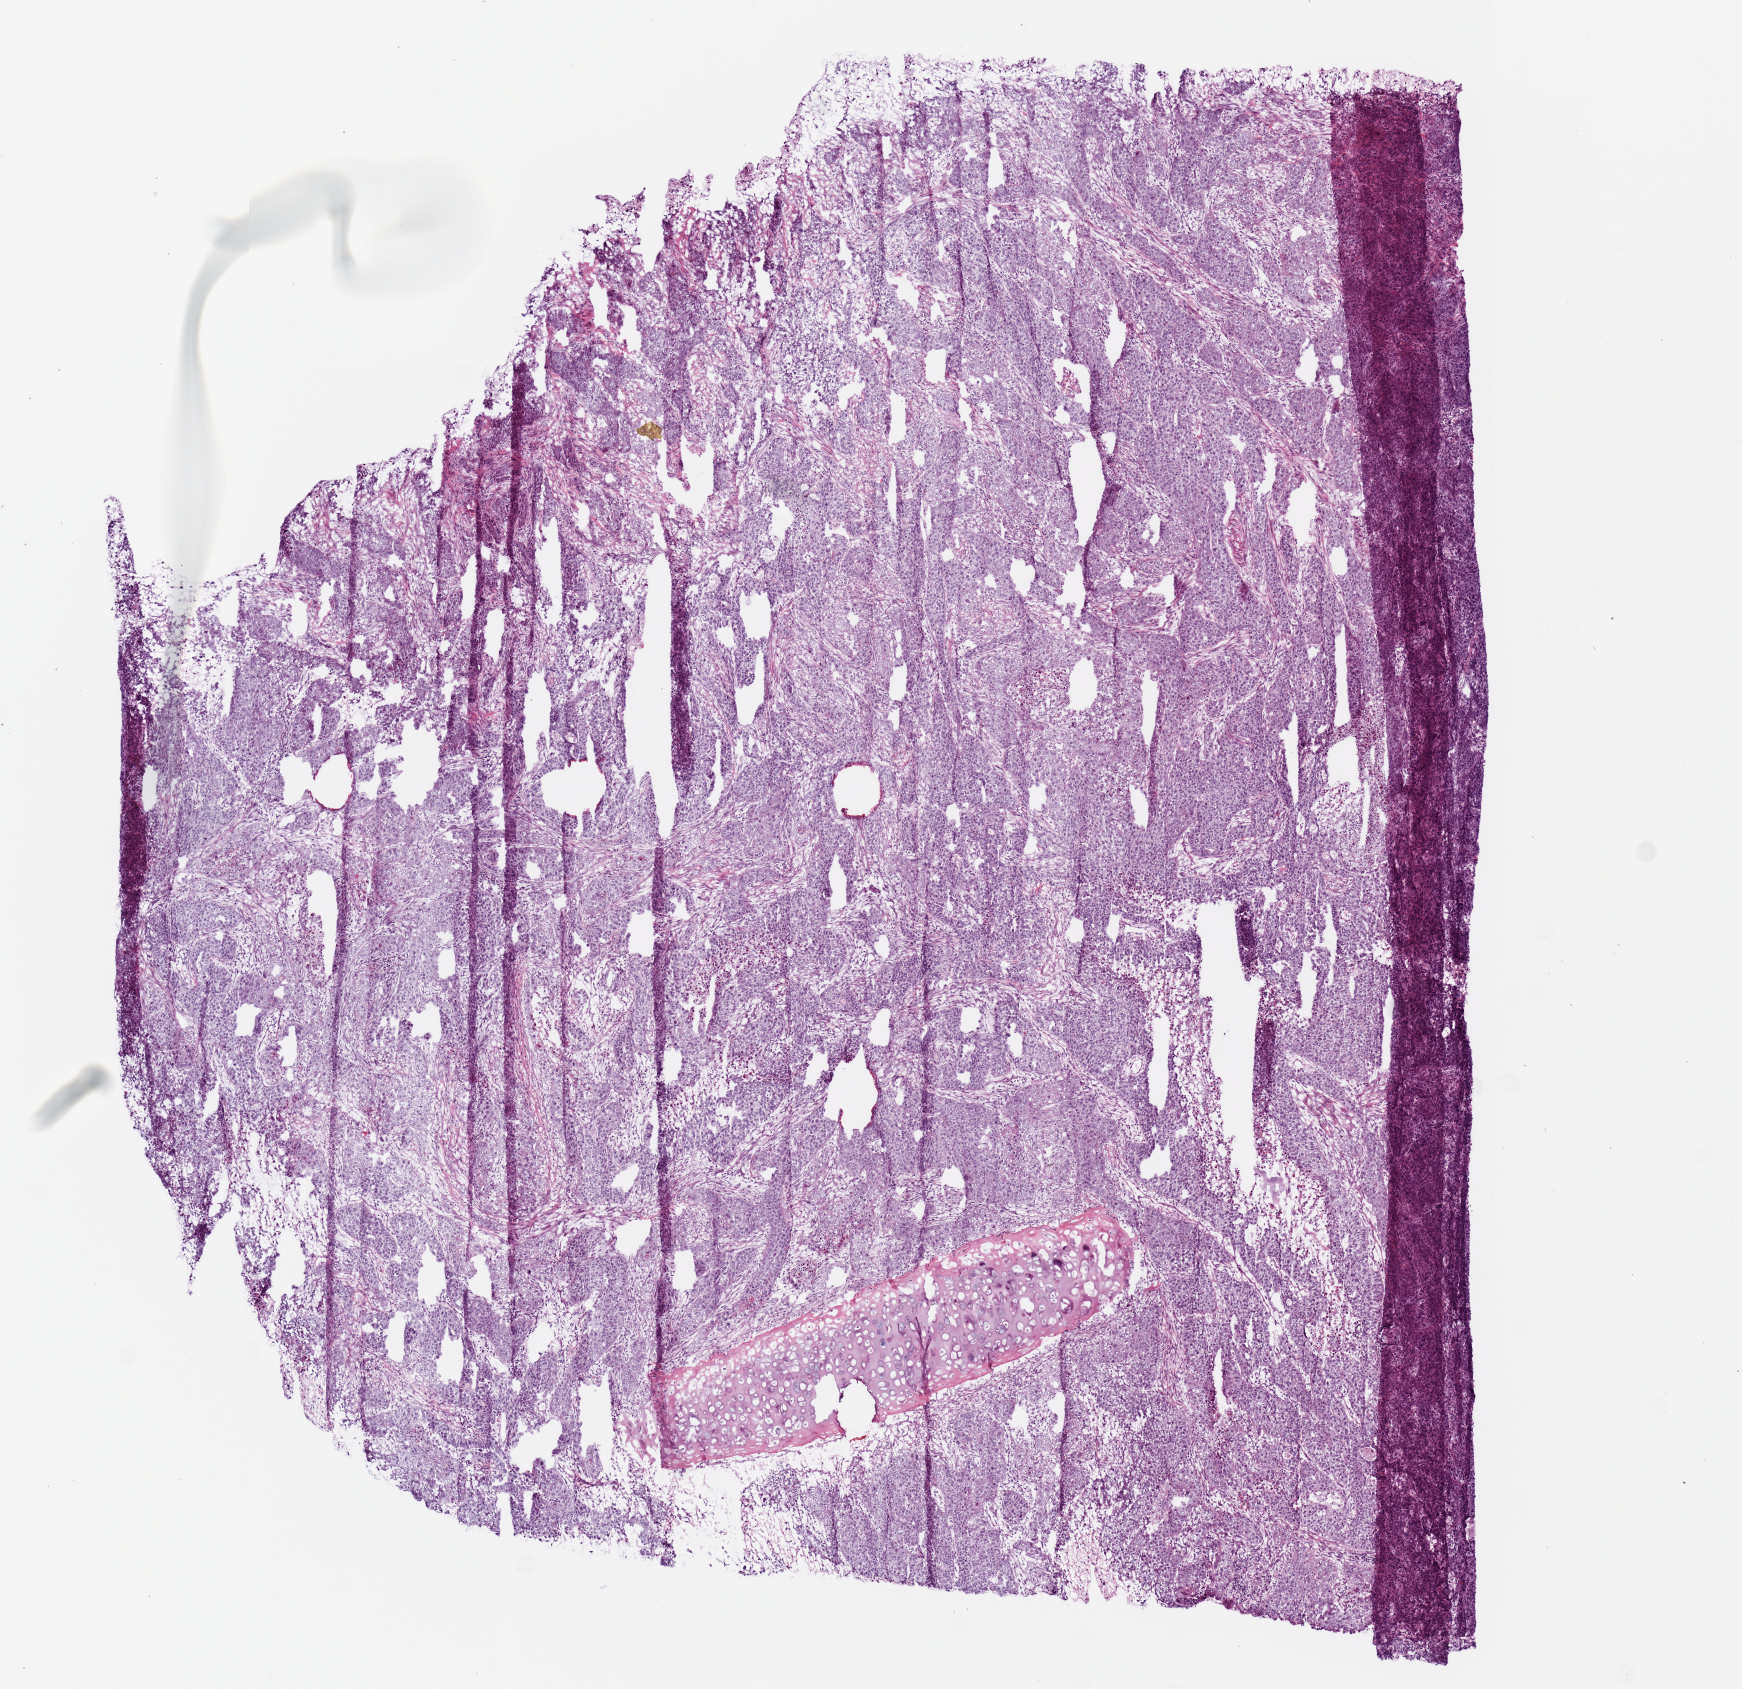
Whole-slide histology image, H&E-stained, low-resolution overview of the scanned area, about 6.9 x 6.7 mm (from a 20x scan); frozen section; primary tumour sample from the lung. Male patient; age at initial diagnosis 63 years. Slide review estimates, as recorded: tumour cells 100%, tumour nuclei 80%, normal cells 0%, stromal cells 0%, necrosis 0%. Inflammatory infiltration, as recorded: lymphocyte infiltration 5%, monocyte infiltration 0%, neutrophil infiltration 7%.
• AJCC pathologic stage: IIA (7th edition)
• pathologic diagnosis: Squamous cell carcinoma, NOS (lower lobe, lung)